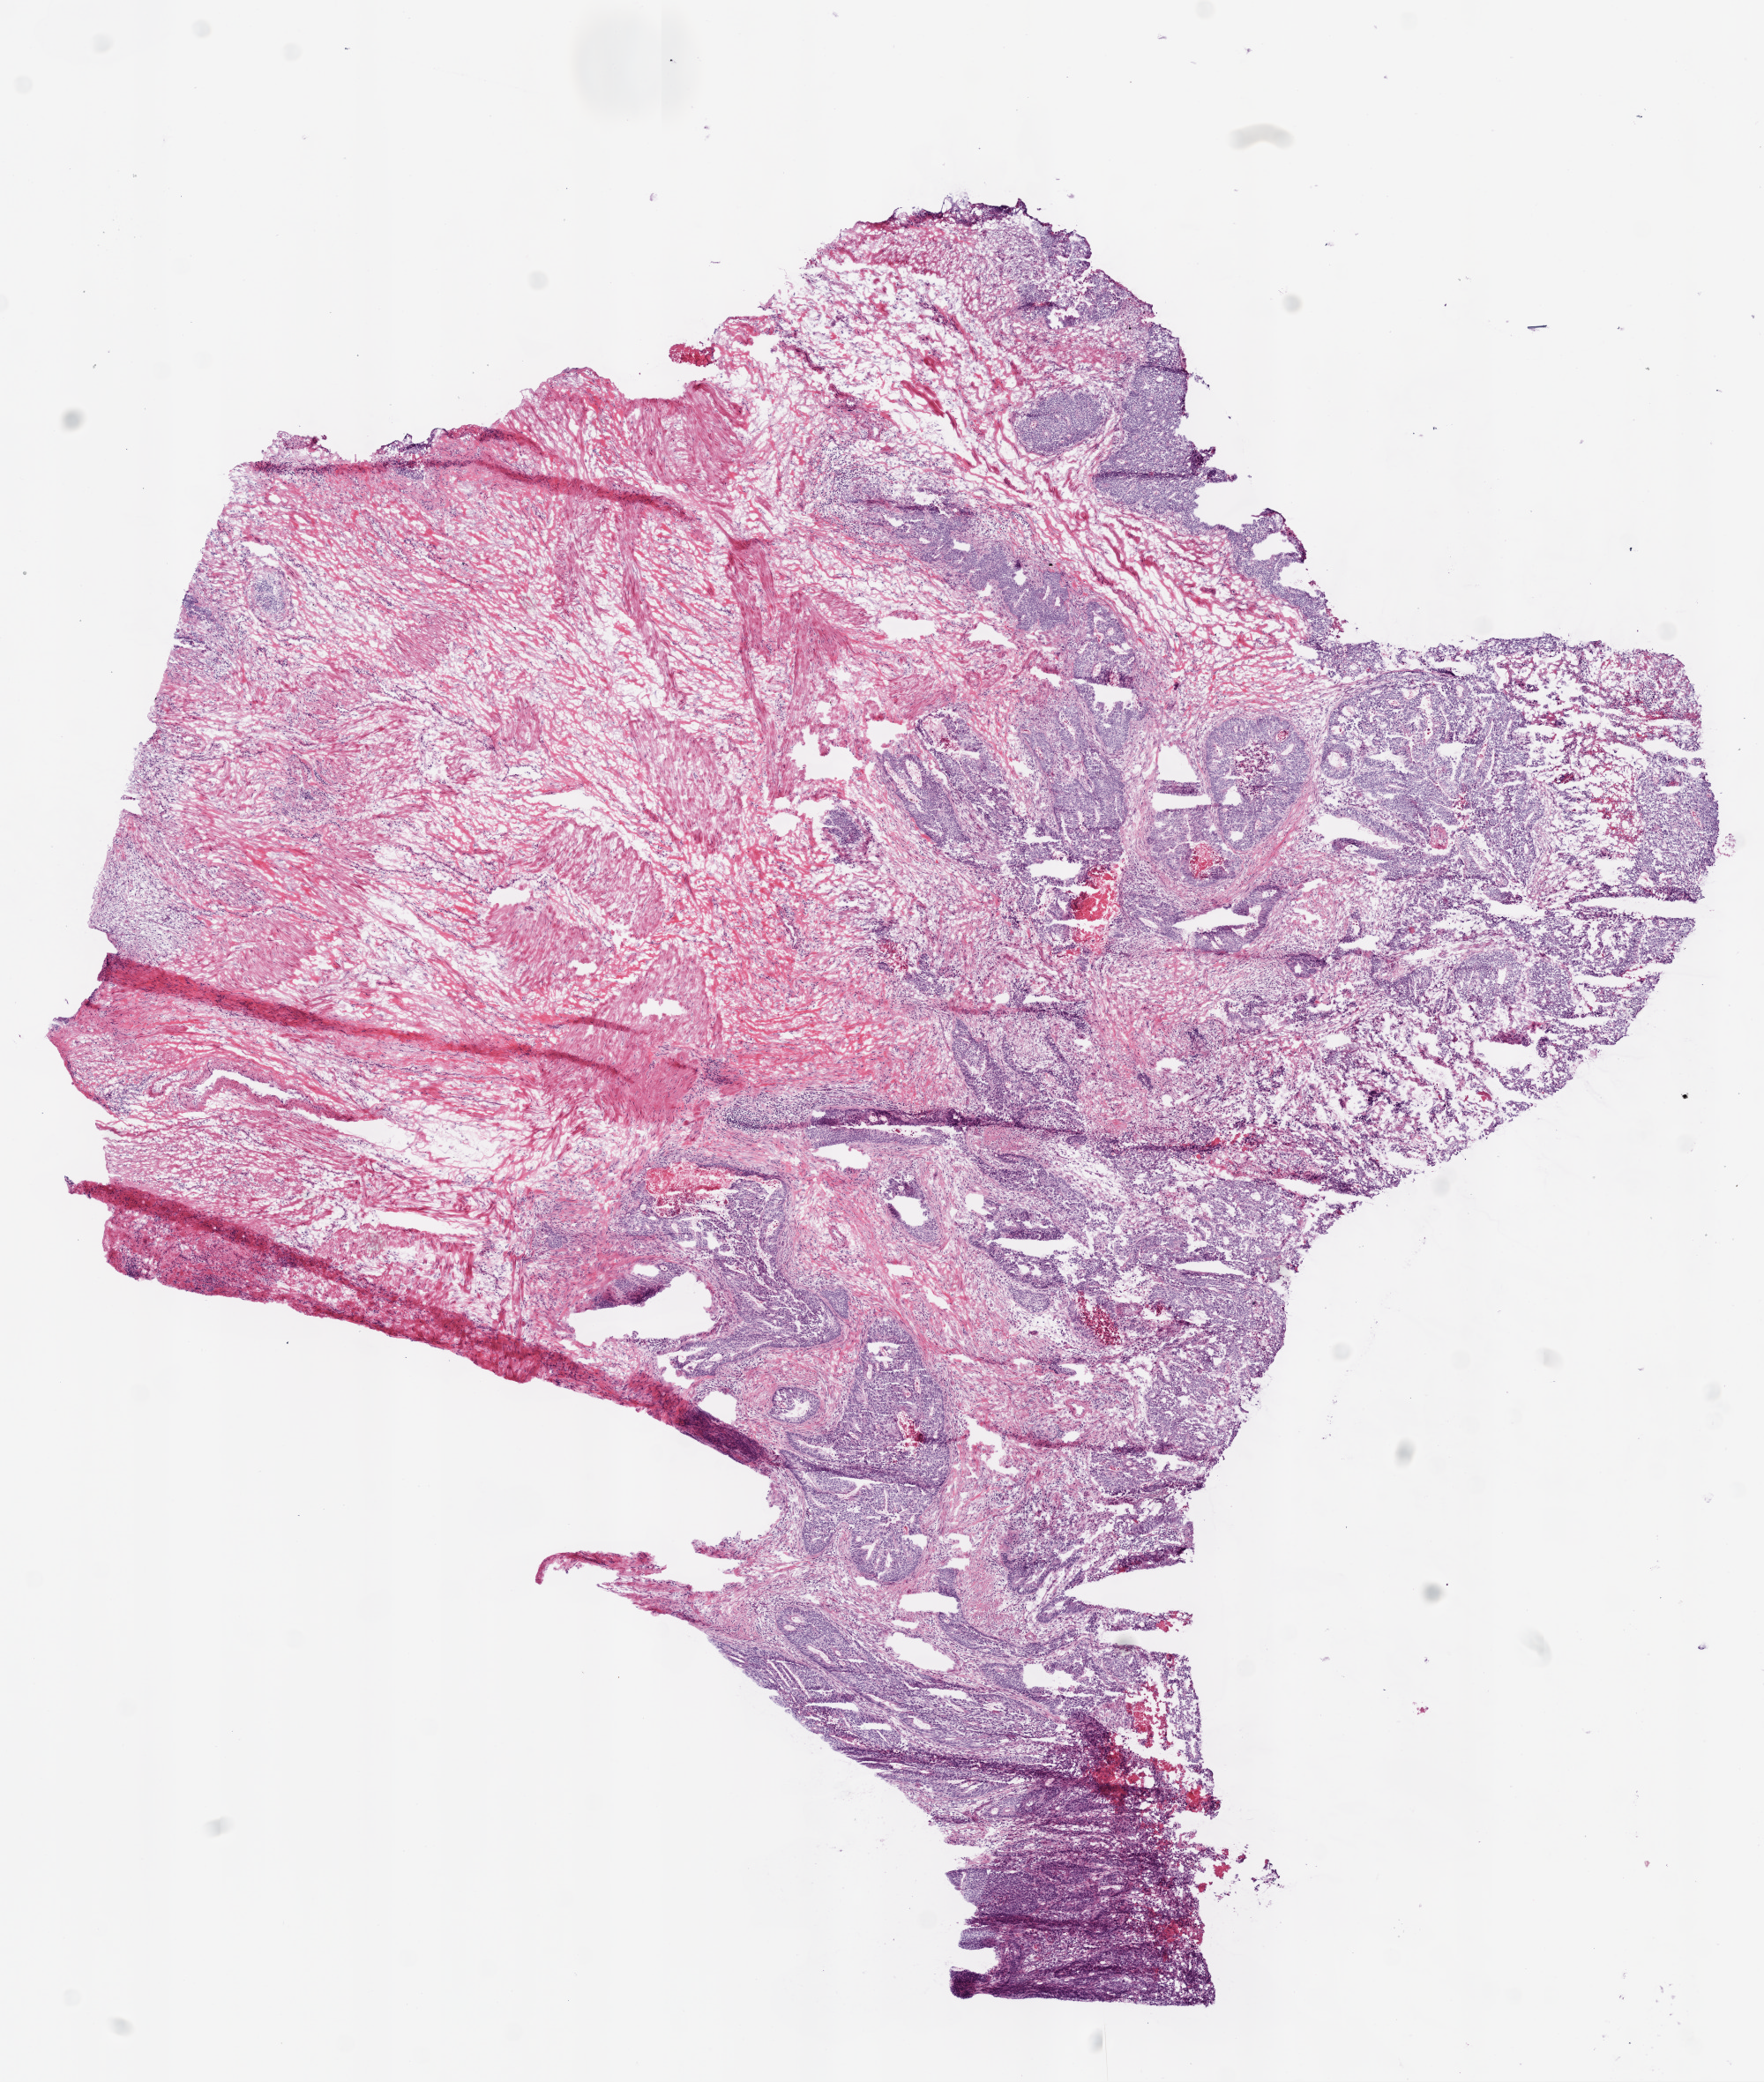
Whole-slide histology image, H&E, whole scanned area (about 8.0 x 9.5 mm, slide scanned at 20x) shown as a low-resolution overview, frozen section, primary tumour sample from the colon. Female patient; age at initial diagnosis 81 years. Composition of this section per pathologist review: tumour cells 70%, tumour nuclei 70%, normal cells 0%, stromal cells 30%, necrosis 0%.
* AJCC pathologic stage: I (6th edition)
* pathologic diagnosis: Adenocarcinoma, NOS